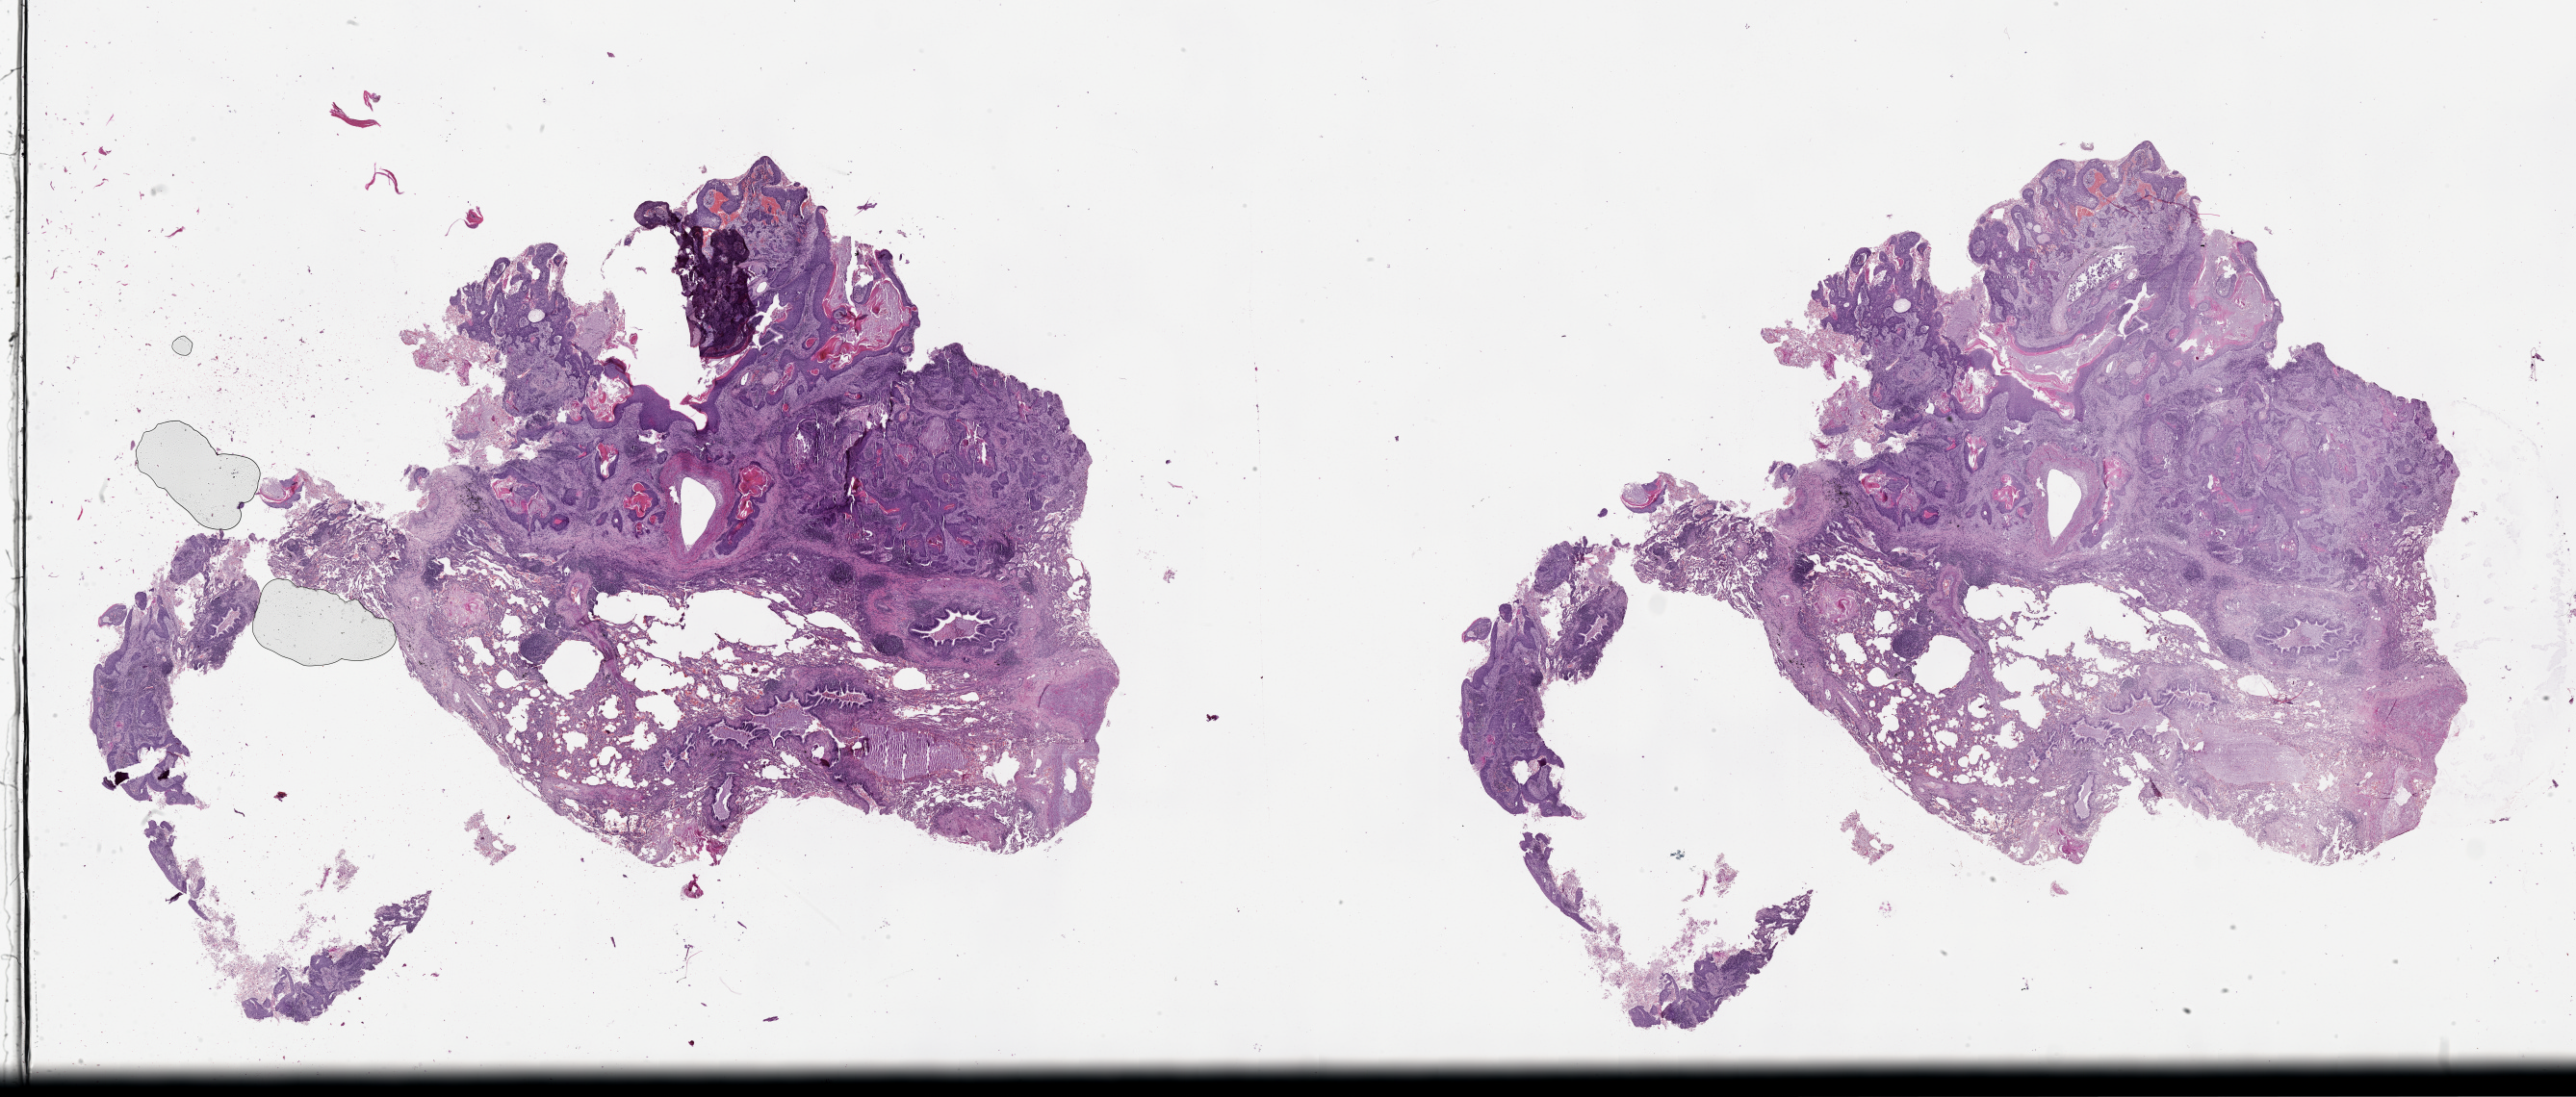
H&E-stained whole-slide image, whole scanned area (about 43.1 x 18.4 mm) shown as a low-resolution overview, tumour tissue sample, lung. Patient: male, age 72 years.
Patient diagnosis (cohort enrolment): squamous cell carcinoma (lung).